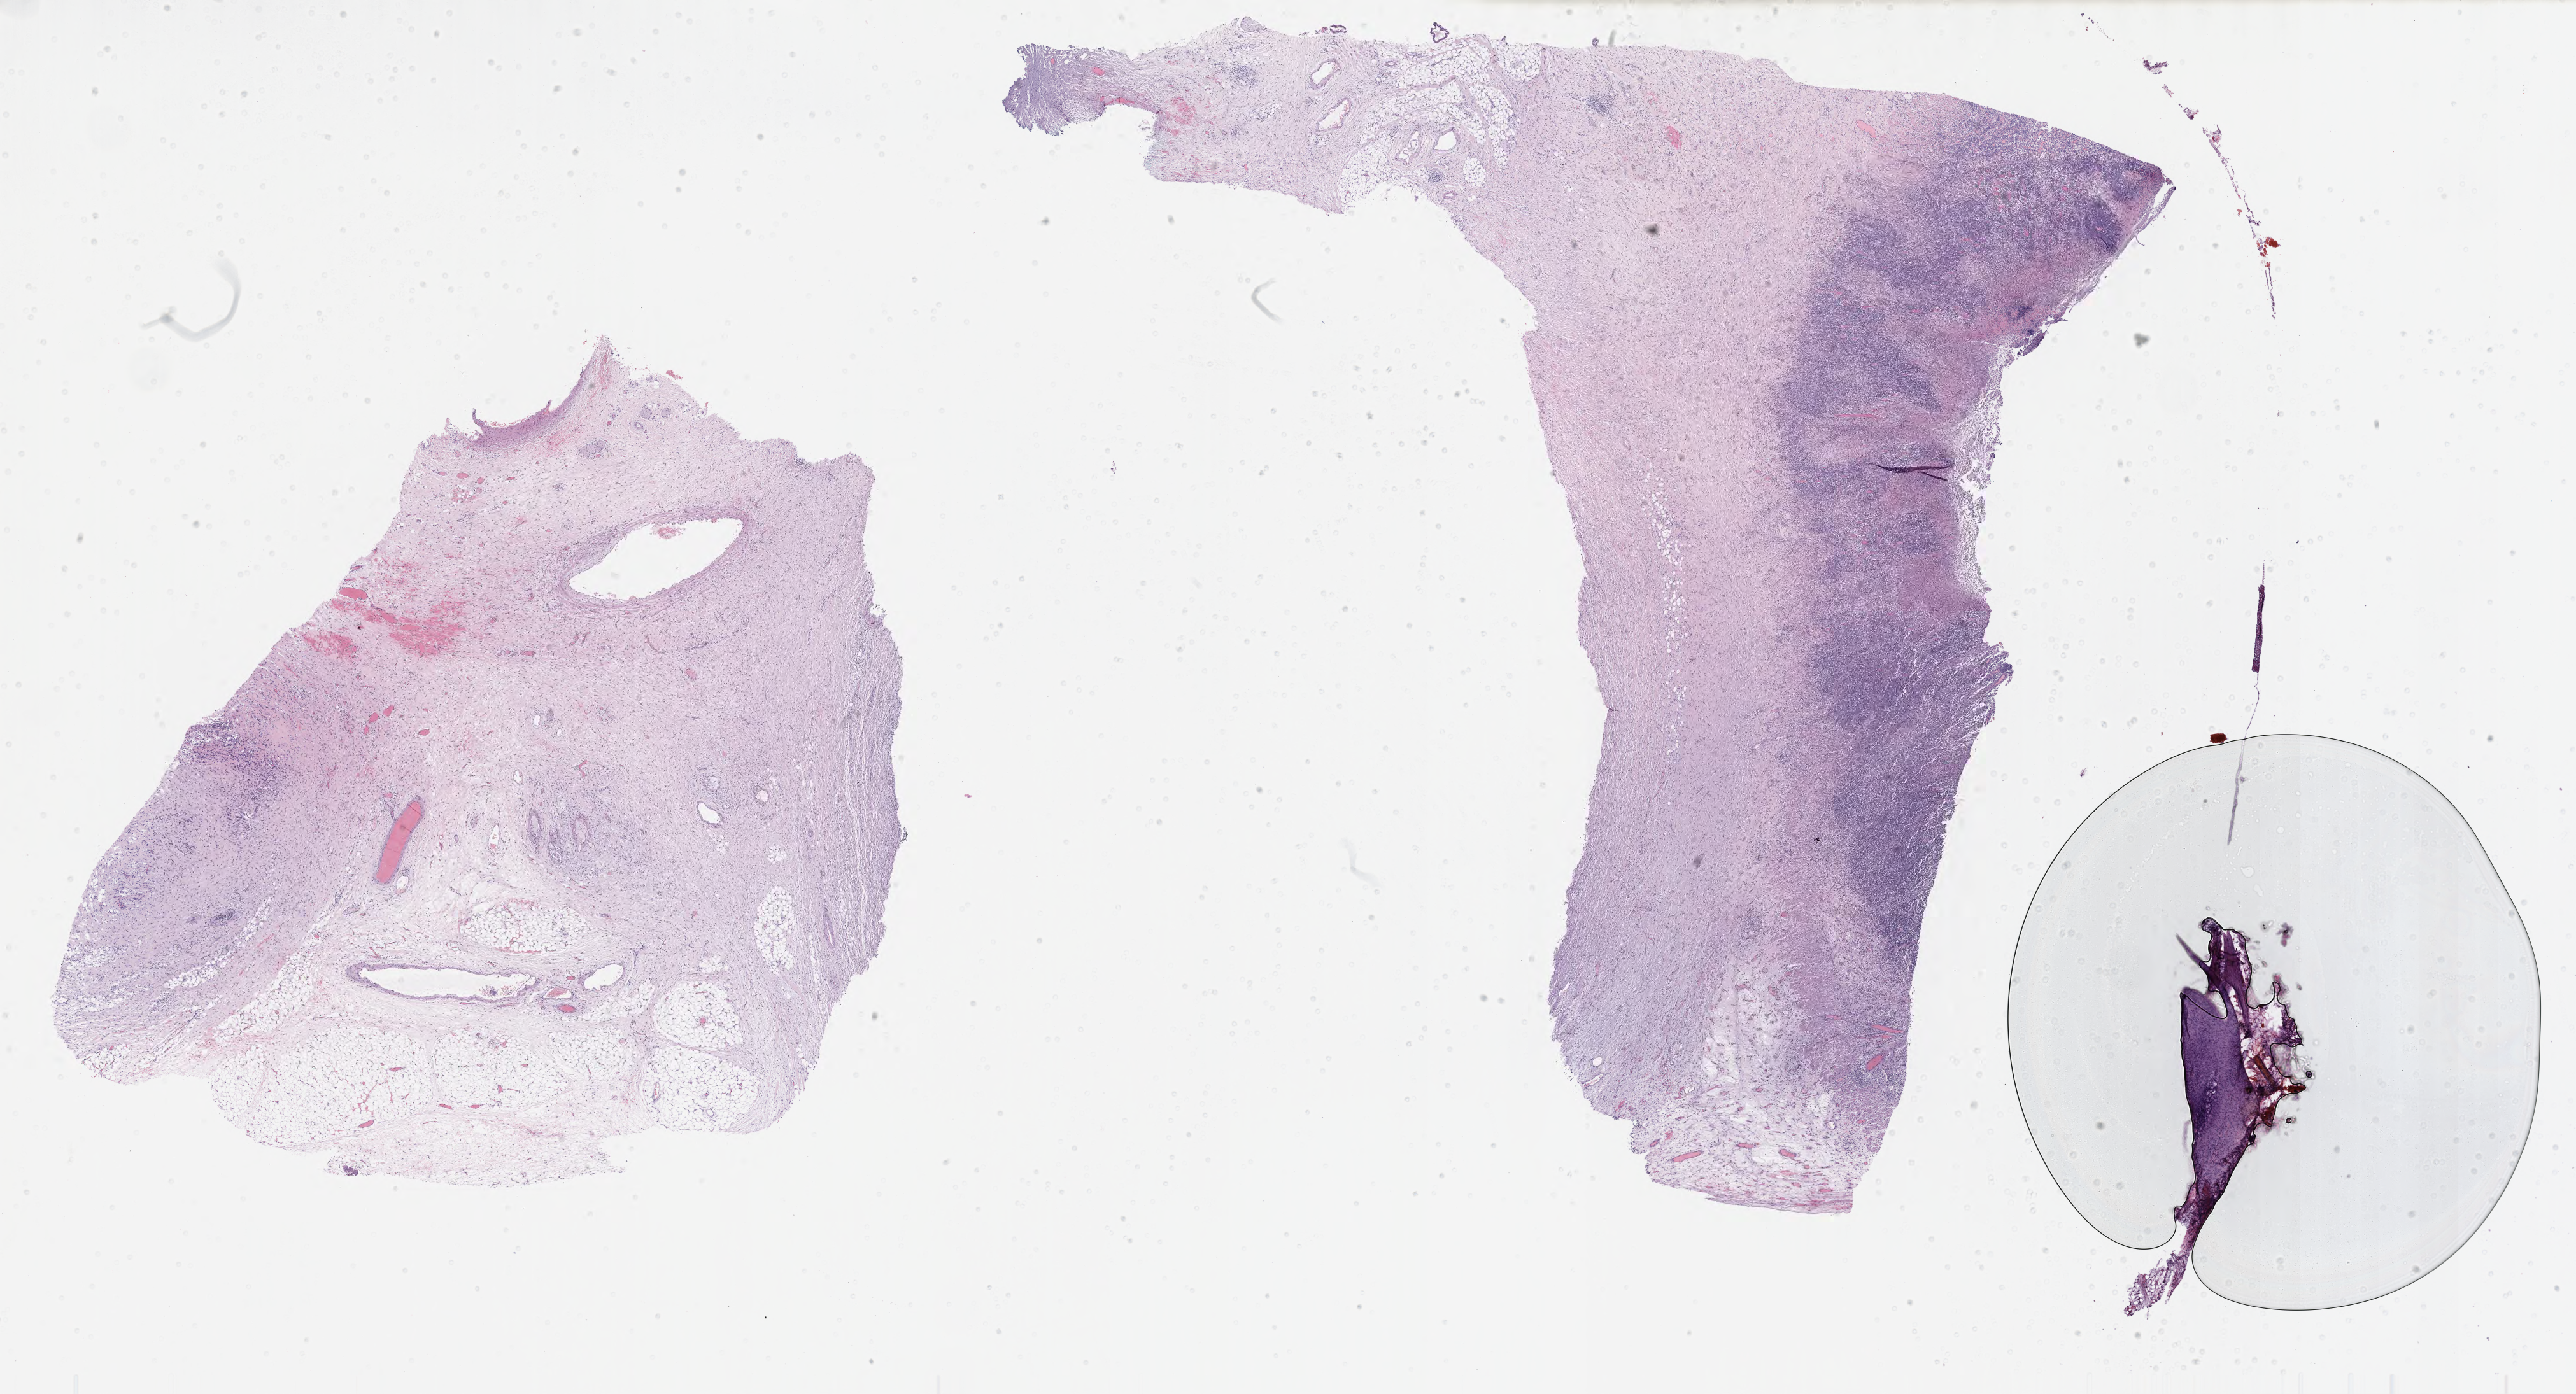
Hematoxylin and eosin (H&E) whole-slide image — a low-resolution overview of the entire scanned area, about 32.7 x 17.7 mm. Tumor tissue. Patient: female, 44 years old.
- diagnosis: Burkitt lymphoma, NOS